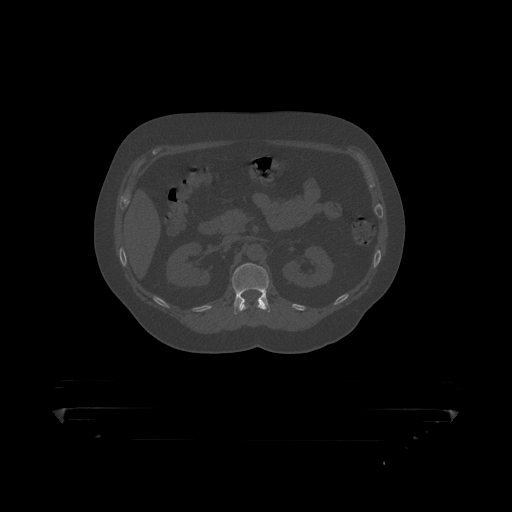
CT including the spine, one axial slice; position 154 of 390 along the scan axis; reconstruction kernel STANDARD; 120 kVp; bone window (W 1800 / L 400 HU); 1.25 mm slice thickness; 512 × 512 image matrix, field of view 650 × 650 mm. Patient: male, 60 years. Case-level facts recorded for this patient, not image findings: primary cancer: prostate.
Structures marked on this image (semi-automatically segmented with operator editing):
- L1 vertebra: bounding box (x1, y1, x2, y2) in pixels: (232, 263, 271, 315)
- T12 vertebra: (237, 300, 269, 314)